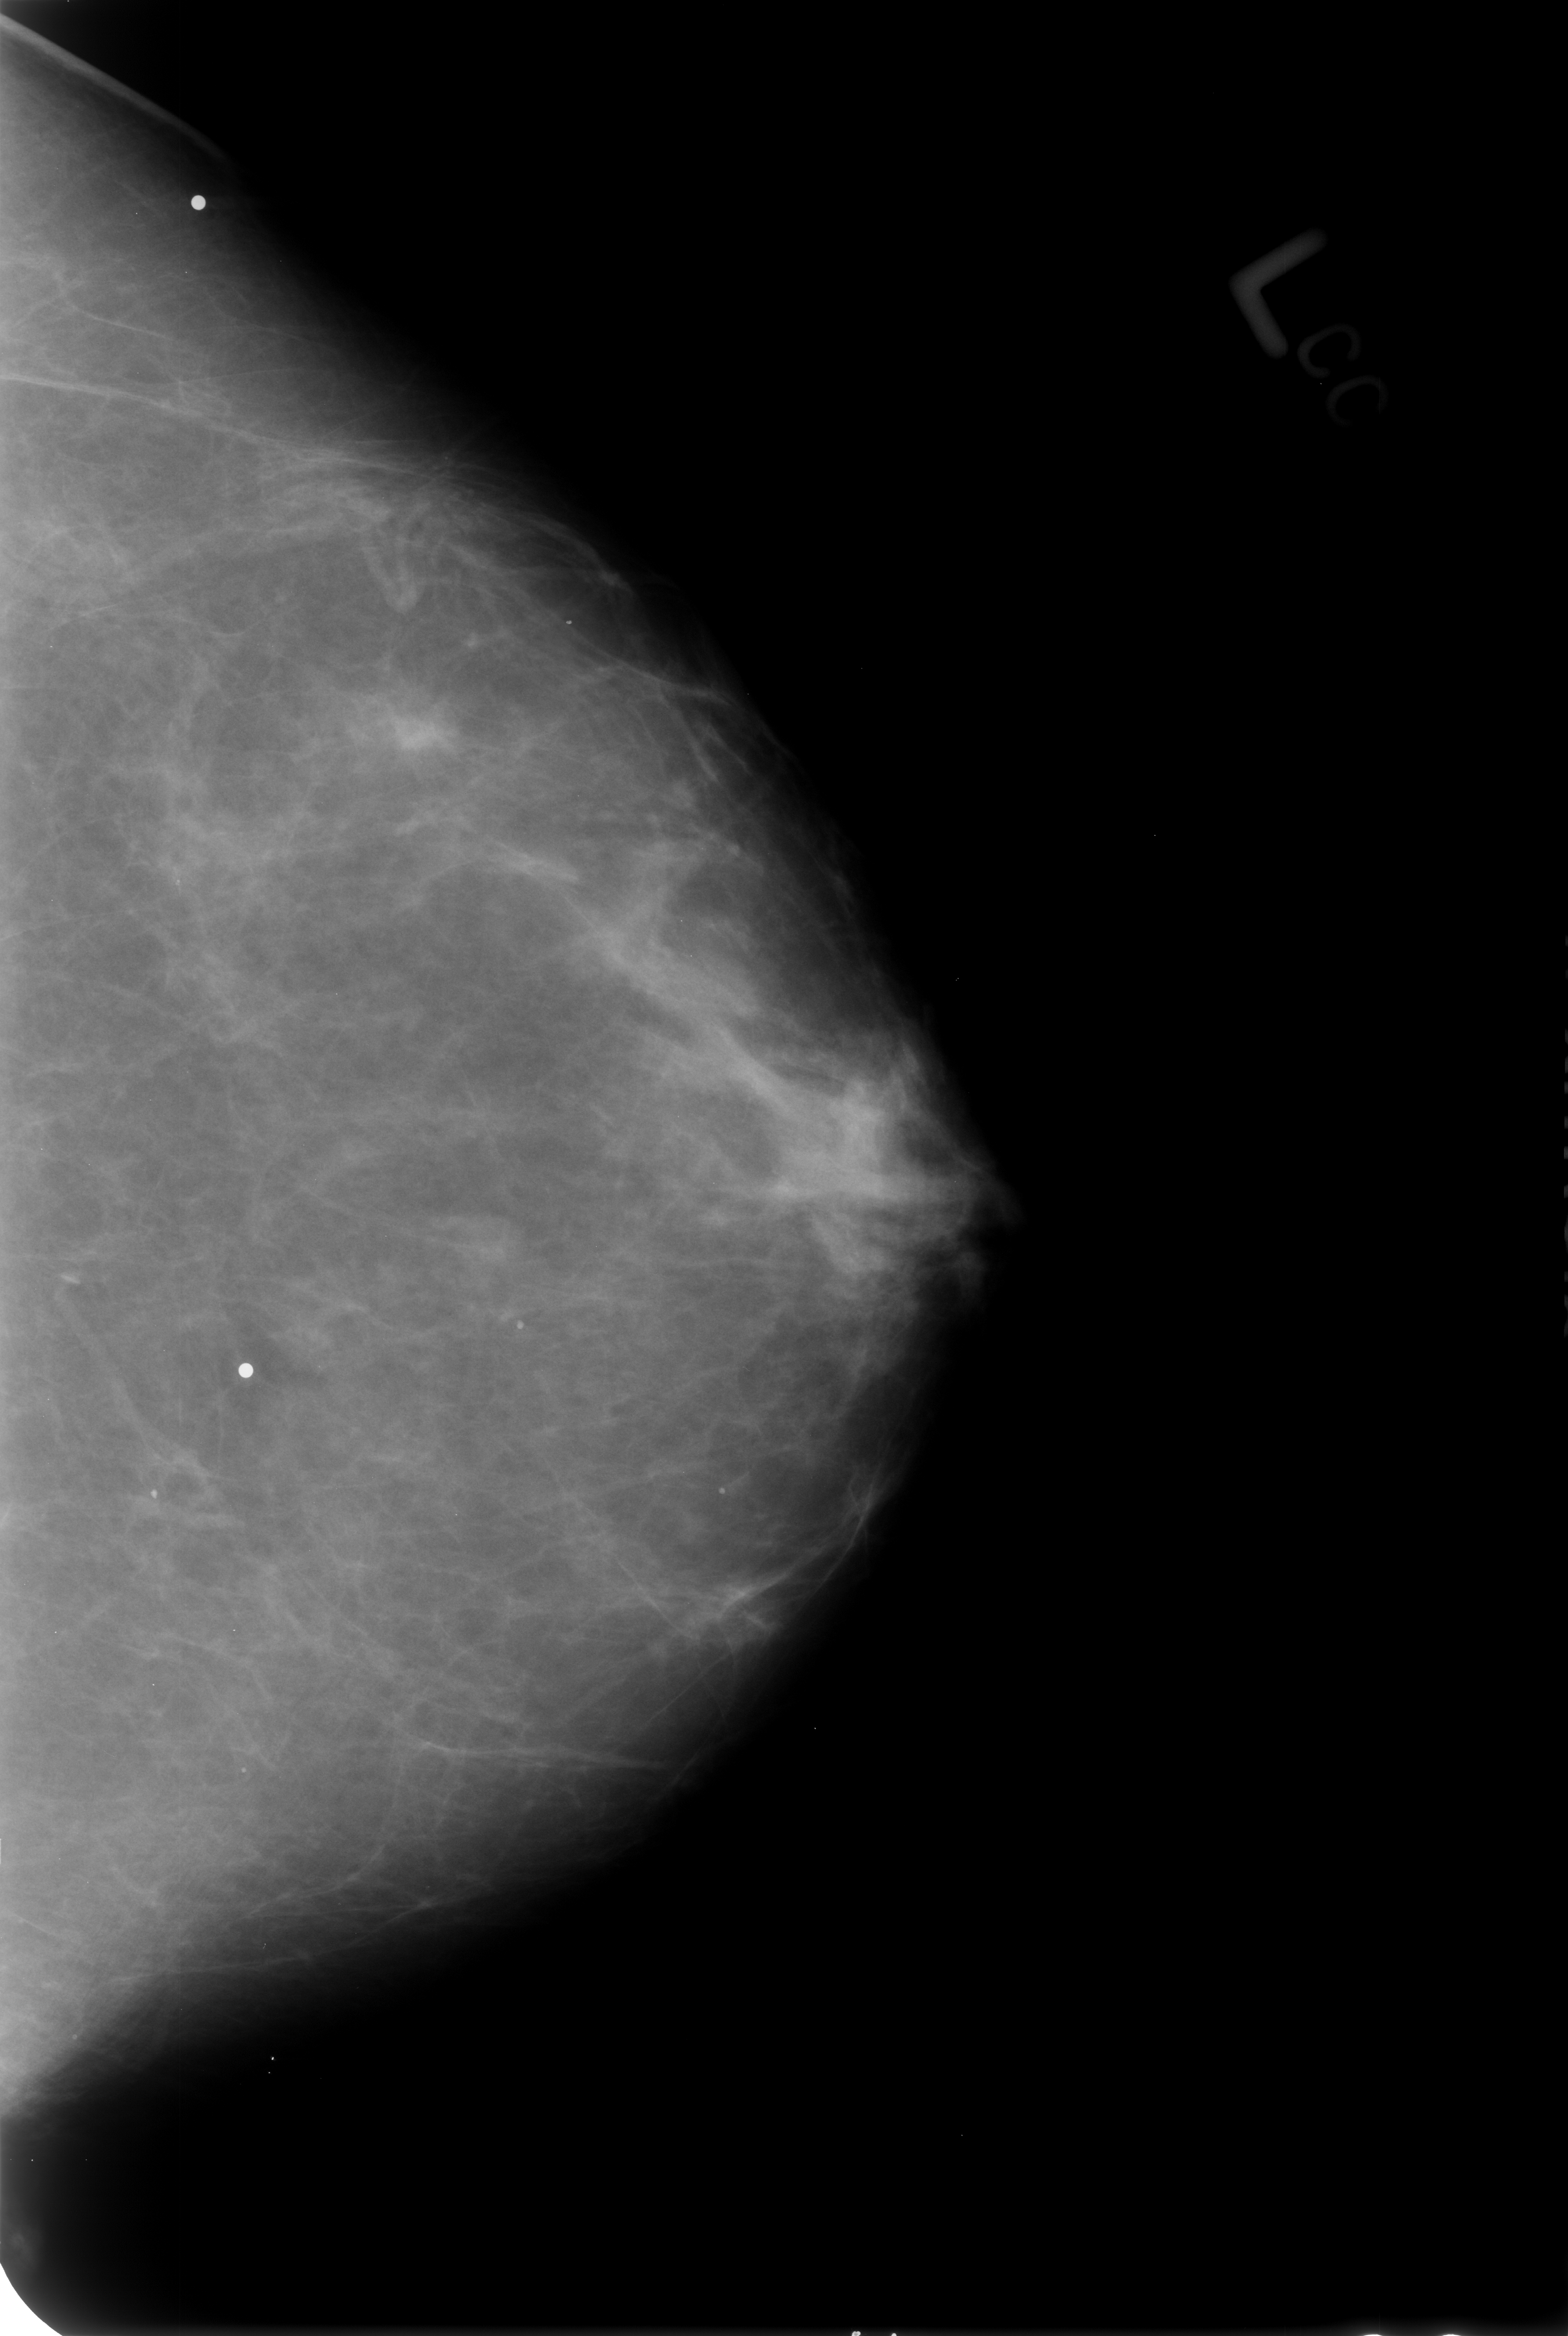
Scanned film-screen mammogram, left breast, craniocaudal (CC) view, BI-RADS breast density category 2 (scale 1–4).
- Abnormality record for this image: Finding 1 of 3: calcifications, morphology punctate; BI-RADS assessment category 2; benign; no additional work-up was recommended (benign without callback).
- Finding 2 of 3: calcifications, morphology punctate; BI-RADS assessment category 2; benign; no additional work-up was recommended (benign without callback).
- Finding 3 of 3: calcifications, morphology punctate; BI-RADS assessment category 2; benign without callback (not worked up further).